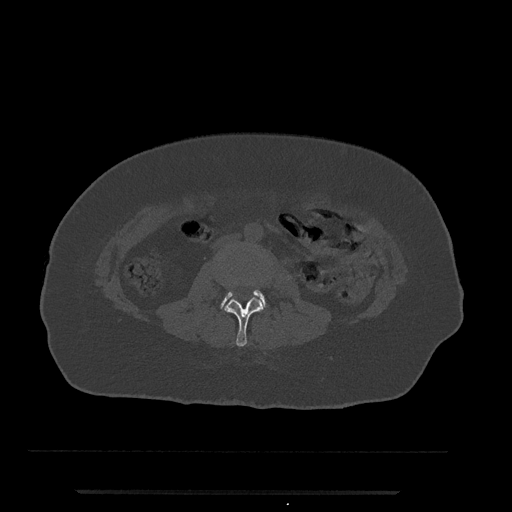
CT including the spine, one axial slice. Position 7 of 797 along the scan axis. Reconstruction kernel Br40s/3. 120 kVp. Bone window (W 1800 / L 400 HU). 512 × 512 image matrix, field of view 440 × 440 mm. Female patient, age 51 years. From the clinical record (not read from this slice): primary cancer: neuro.
Annotated regions visible in this slice (semi-automatically segmented with operator editing):
- L2 vertebra: bounding box [x1, y1, x2, y2] px = [225, 279, 266, 347]